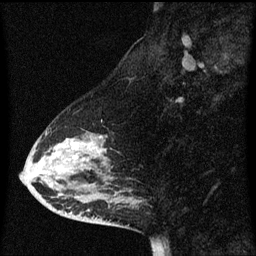
Breast MRI (dynamic contrast-enhanced), one sagittal slice. Position 26 of 60 along the scan axis. Dynamic contrast-enhanced series, image 2 of 3 at this slice position (ordered by acquisition). 1.5 T. TE 4.2 ms, TR 8.4 ms. 256 × 256 image matrix. Patient: female, 47 years. Case-level facts recorded for this patient, not image findings: setting: breast cancer imaged before/during neoadjuvant chemotherapy; receptor status: HER2-positive.
Structures marked on this image (semi-automatic segmentation, software-assisted and operator-edited):
- analysis volume of interest (the breast-tissue region the enhancement analysis was run in; not a lesion): box from (x=26, y=122) to (x=137, y=201) px
- tumour enhancement mask (voxels above the 70 % enhancement threshold inside the analysis volume of interest): (x=59, y=136)–(x=102, y=159)